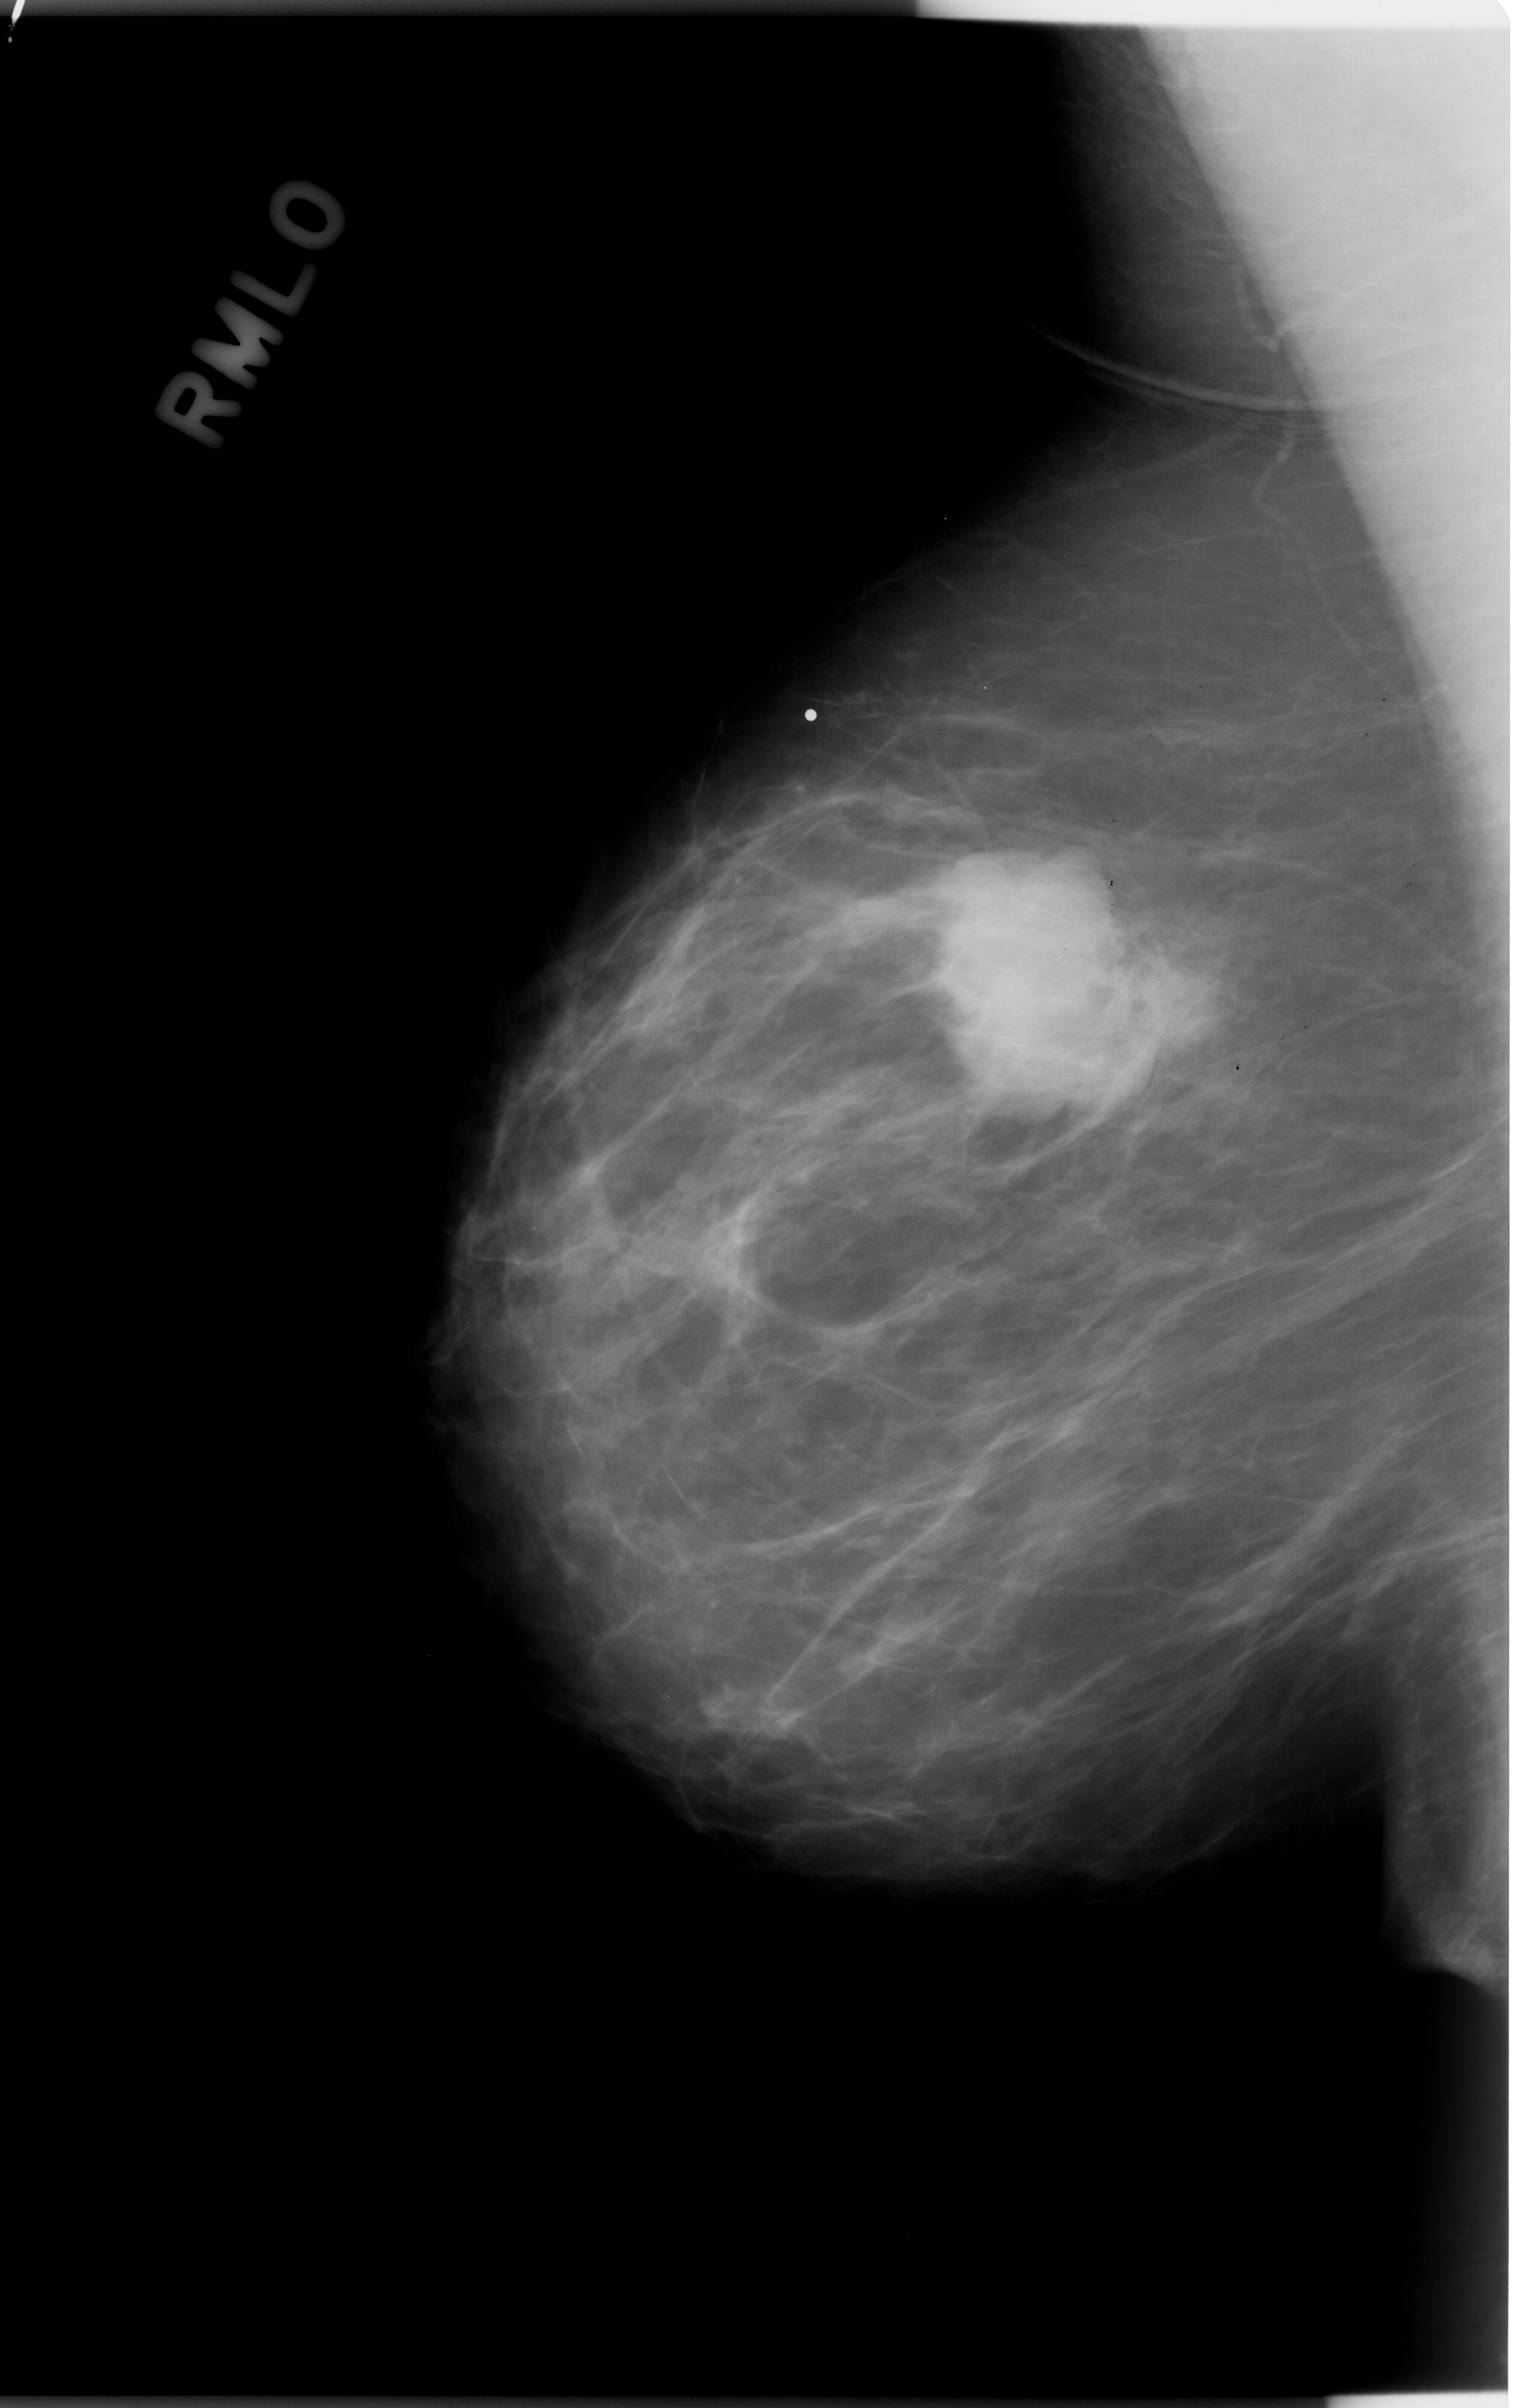
Mammogram (digitized film); right breast; MLO view.
Finding: mass, shape lobulated, margins microlobulated; BI-RADS assessment category 5; pathology result (as recorded, not read from the image): malignant.